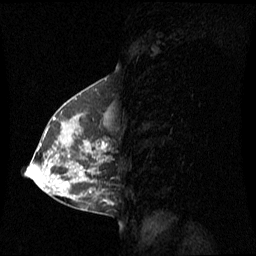
Breast MRI (dynamic contrast-enhanced), one sagittal slice; slice 30 of 60 in the series (ordered by position); dynamic contrast-enhanced series, image 2 of 3 at this slice position (ordered by acquisition); 1.5 T; TE 4.2 ms, TR 8.4 ms; 256 × 256 image matrix, field of view 270 × 270 mm. Patient: female, 42 years. Case-level facts recorded for this patient, not image findings: setting: breast cancer imaged before/during neoadjuvant chemotherapy; receptor status: HR-positive, HER2-negative.
Annotated regions visible in this slice (semi-automatic segmentation, software-assisted and operator-edited):
- analysis volume of interest (the breast-tissue region the enhancement analysis was run in; not a lesion): box from (x=56, y=114) to (x=109, y=185) px
- tumour enhancement mask (voxels above the 70 % enhancement threshold inside the analysis volume of interest): (x=86, y=142)–(x=106, y=148)